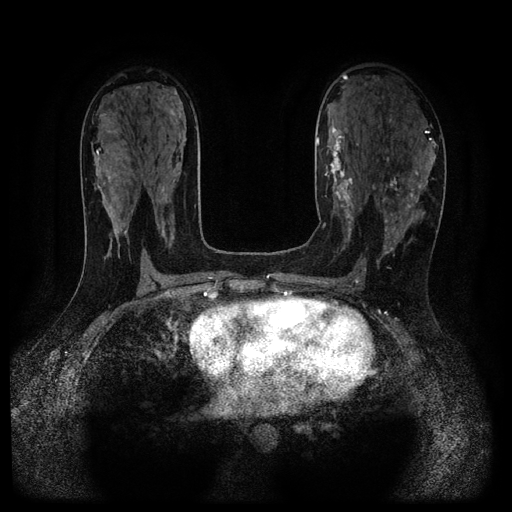
Breast MRI (dynamic contrast-enhanced, multi-phase), one axial slice. Slice 60 of 116 in the series (ordered by position). Dynamic contrast-enhanced series, time point 2 of 5 at this slice position (early post-contrast). 1.5 T. TE 2.7 ms, TR 5.4 ms. 2.2 mm slice thickness. 512 × 512 image matrix. Patient: female, 43 years.
Structures marked on this image (semi-automatic segmentation, software-assisted and operator-edited):
- breast lesion (labelled benign in the annotation): bounding box [x1, y1, x2, y2] px = [322, 122, 356, 245]